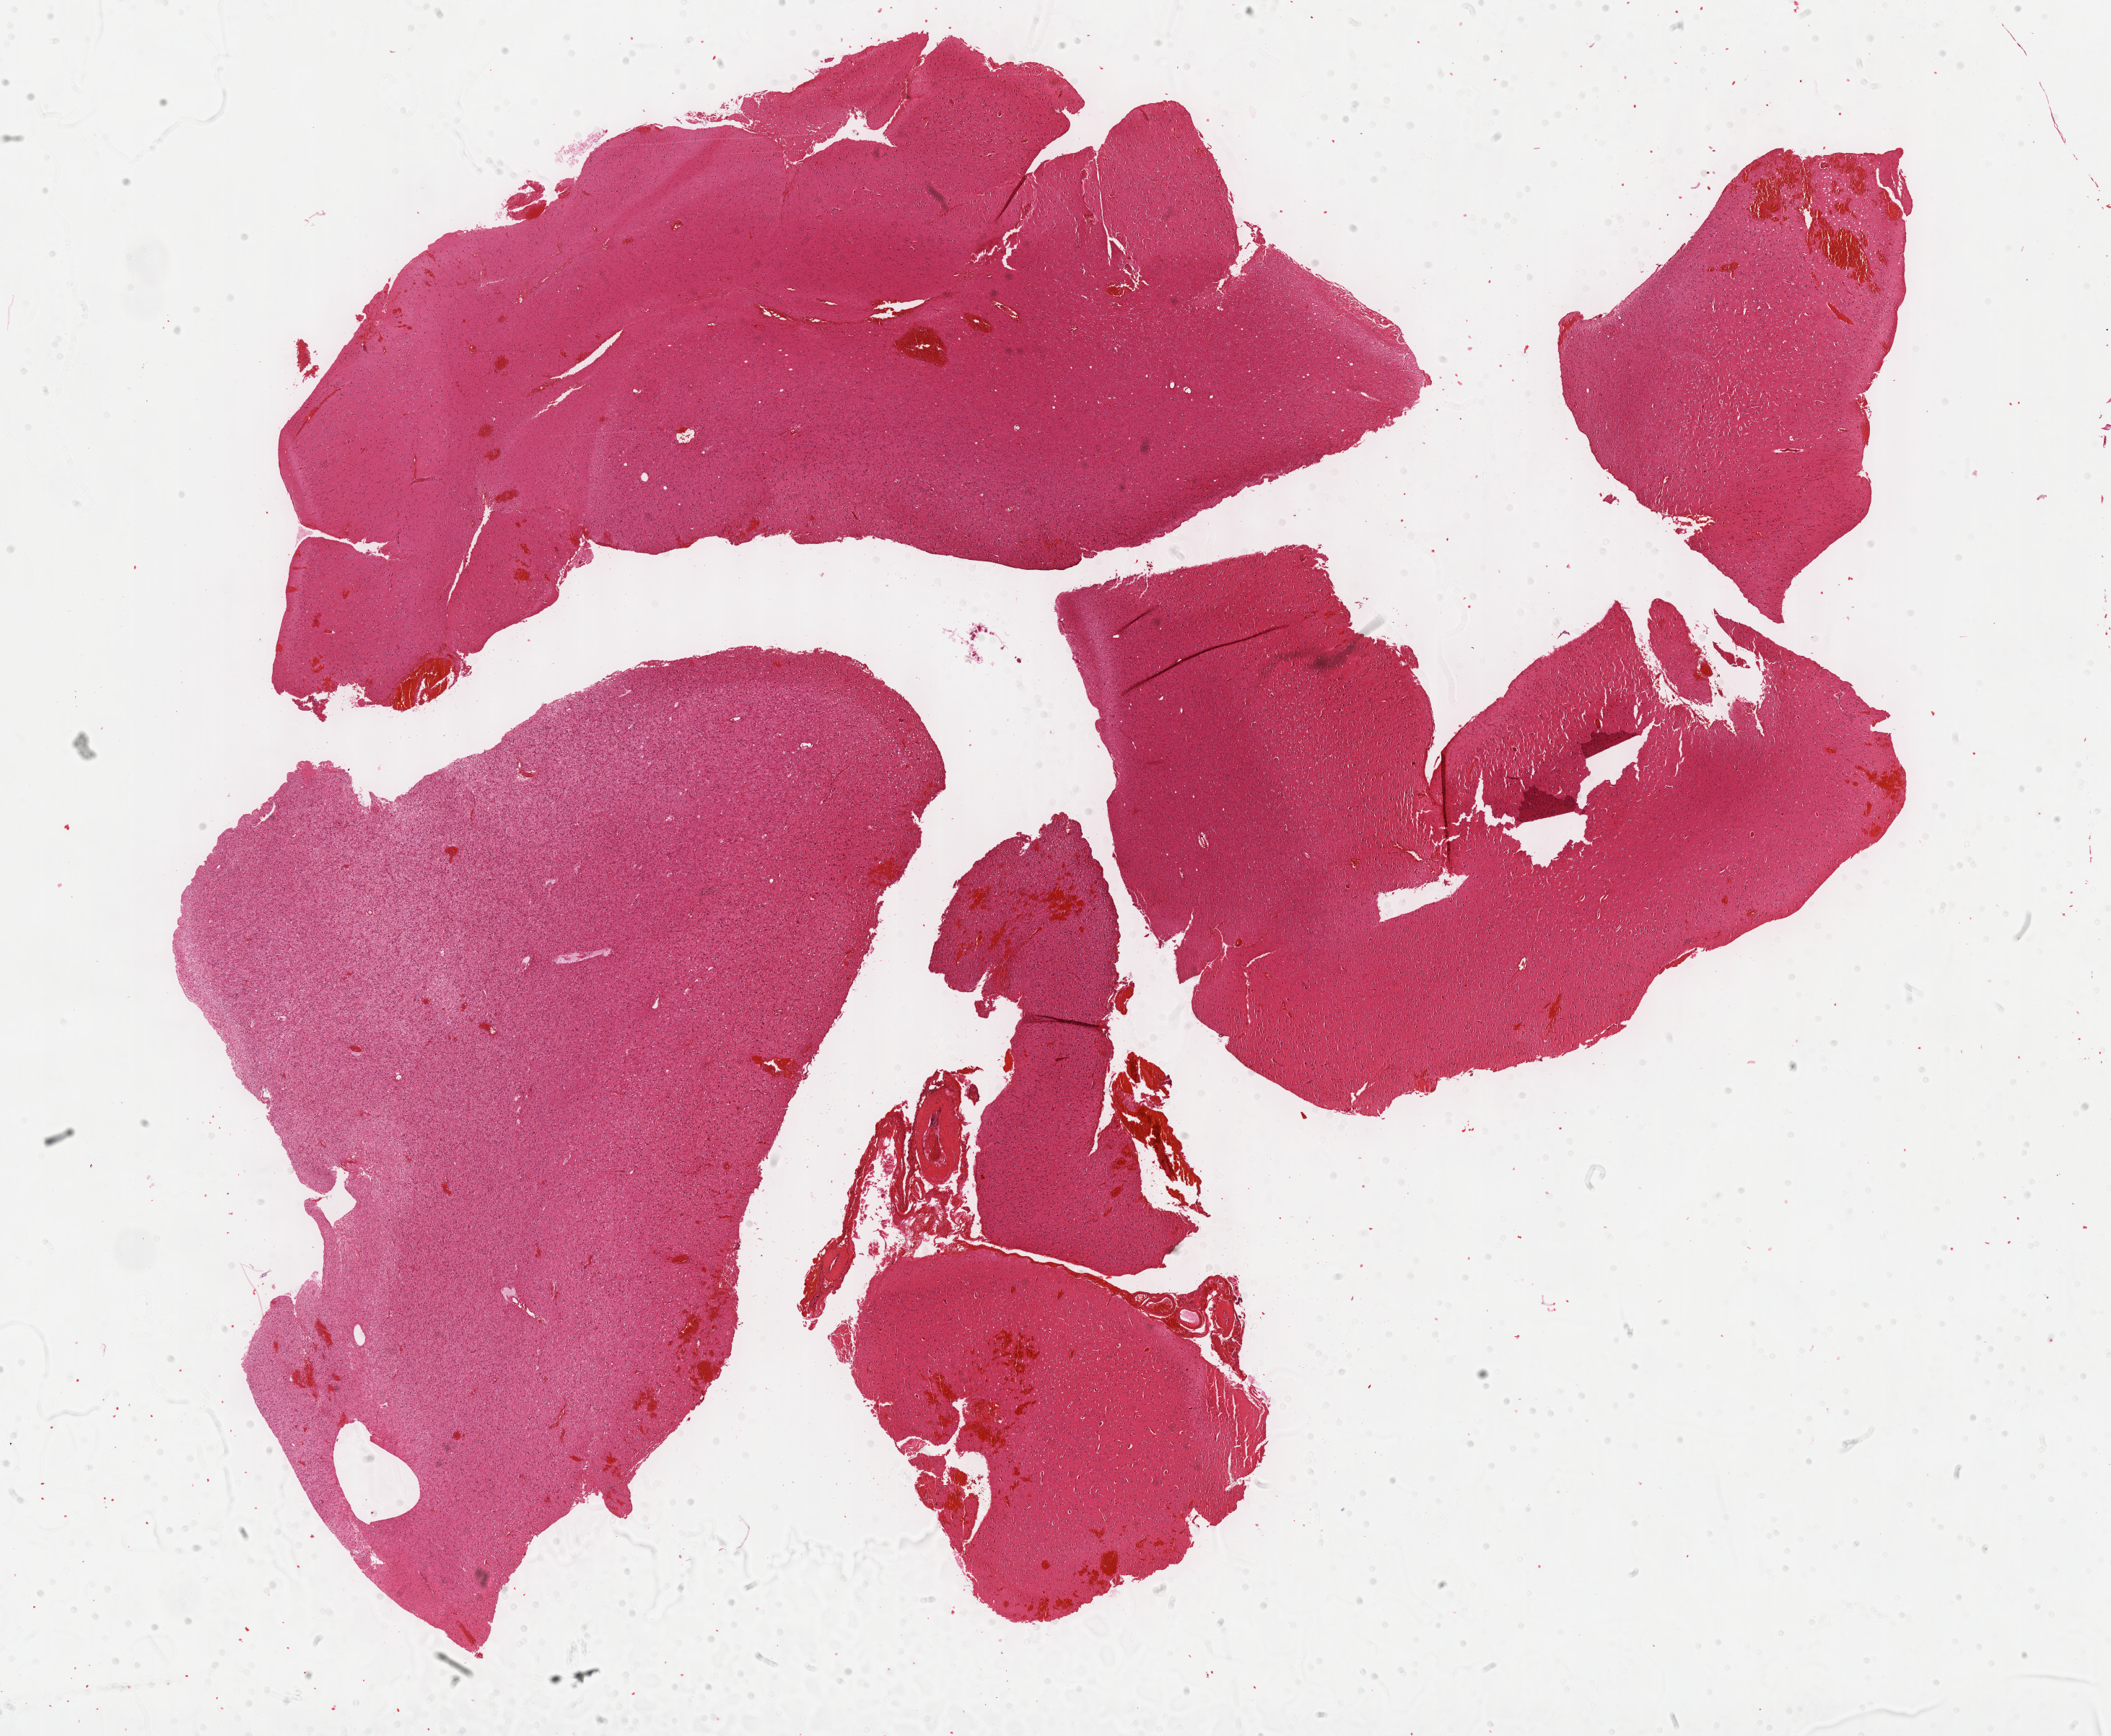
Digitized Hematoxylin and eosin (H&E) stained tissue section (whole slide) — shown as a low-resolution overview of the whole scanned area (about 23.7 x 19.5 mm). Formalin-fixed paraffin-embedded (FFPE) diagnostic section. Brain, primary tumour sample. Male patient; age at initial diagnosis 31 years. Histologic grade: G3 (poorly differentiated).
Diagnosis: Astrocytoma, anaplastic (cerebrum).